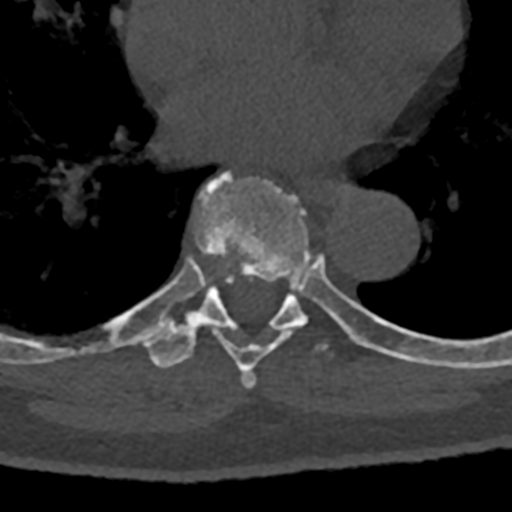
CT including the spine, one axial slice; position 737 of 797 along the scan axis; reconstruction kernel Br40s/3; bone window (W 1800 / L 400 HU); 512 × 512 image matrix. Male patient, age 74 years. Case-level facts recorded for this patient, not image findings: primary cancer: renal.
Structures marked on this image (semi-automatic segmentation, software-assisted and operator-edited):
- T7 vertebra: box from (x=187, y=171) to (x=368, y=389) px
- T8 vertebra: (x=72, y=275)–(x=432, y=368)